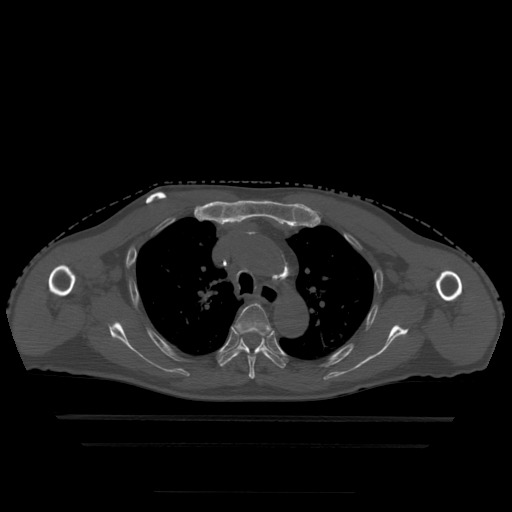
CT including the spine, one axial slice. Slice 346 of 522 in the series (ordered by position). Bone window (W 1800 / L 400 HU). 512 × 512 image matrix. Patient age 68 years. Case-level facts recorded for this patient, not image findings: primary cancer: urothelial.
Annotated regions visible in this slice (semi-automatic segmentation, software-assisted and operator-edited):
- T4 vertebra: bounding box (x1, y1, x2, y2) in pixels: (235, 304, 271, 379)
- T5 vertebra: (219, 330, 286, 369)